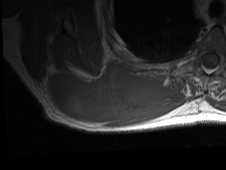
MRI of an extremity soft-tissue mass, one axial slice; slice 27 of 81 in the series (ordered by position); MR volume resampled by the dataset authors to the PET/CT grid (not the native acquisition matrix); 3.27 mm slice thickness; 226 × 170 image matrix. Male patient. Case-level facts recorded for this patient, not image findings: histological type: pleiomorphic spindle cell undifferentiated; grade: high; site of the primary tumour: right parascapusular.
Outlined on this slice (expert contour drawn on MRI and transferred to this co-registered scan by the dataset authors):
- gross tumour volume including surrounding oedema: bounding box (x1, y1, x2, y2) in pixels: (46, 61, 186, 126)
- gross tumour volume (mass): (48, 63, 166, 123)